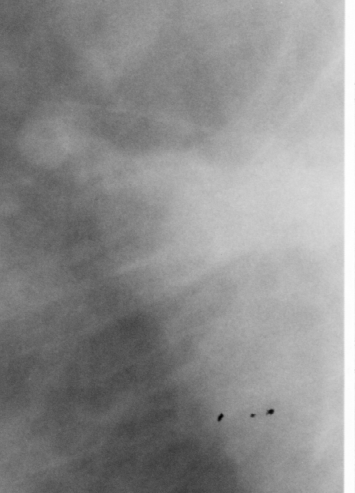
Crop from a digitized film mammogram around one marked abnormality; right breast; MLO view; BI-RADS breast density category 4 (scale 1–4).
- Finding: mass, shape irregular, margins spiculated; BI-RADS assessment category 4; benign; no additional work-up was recommended (benign without callback).